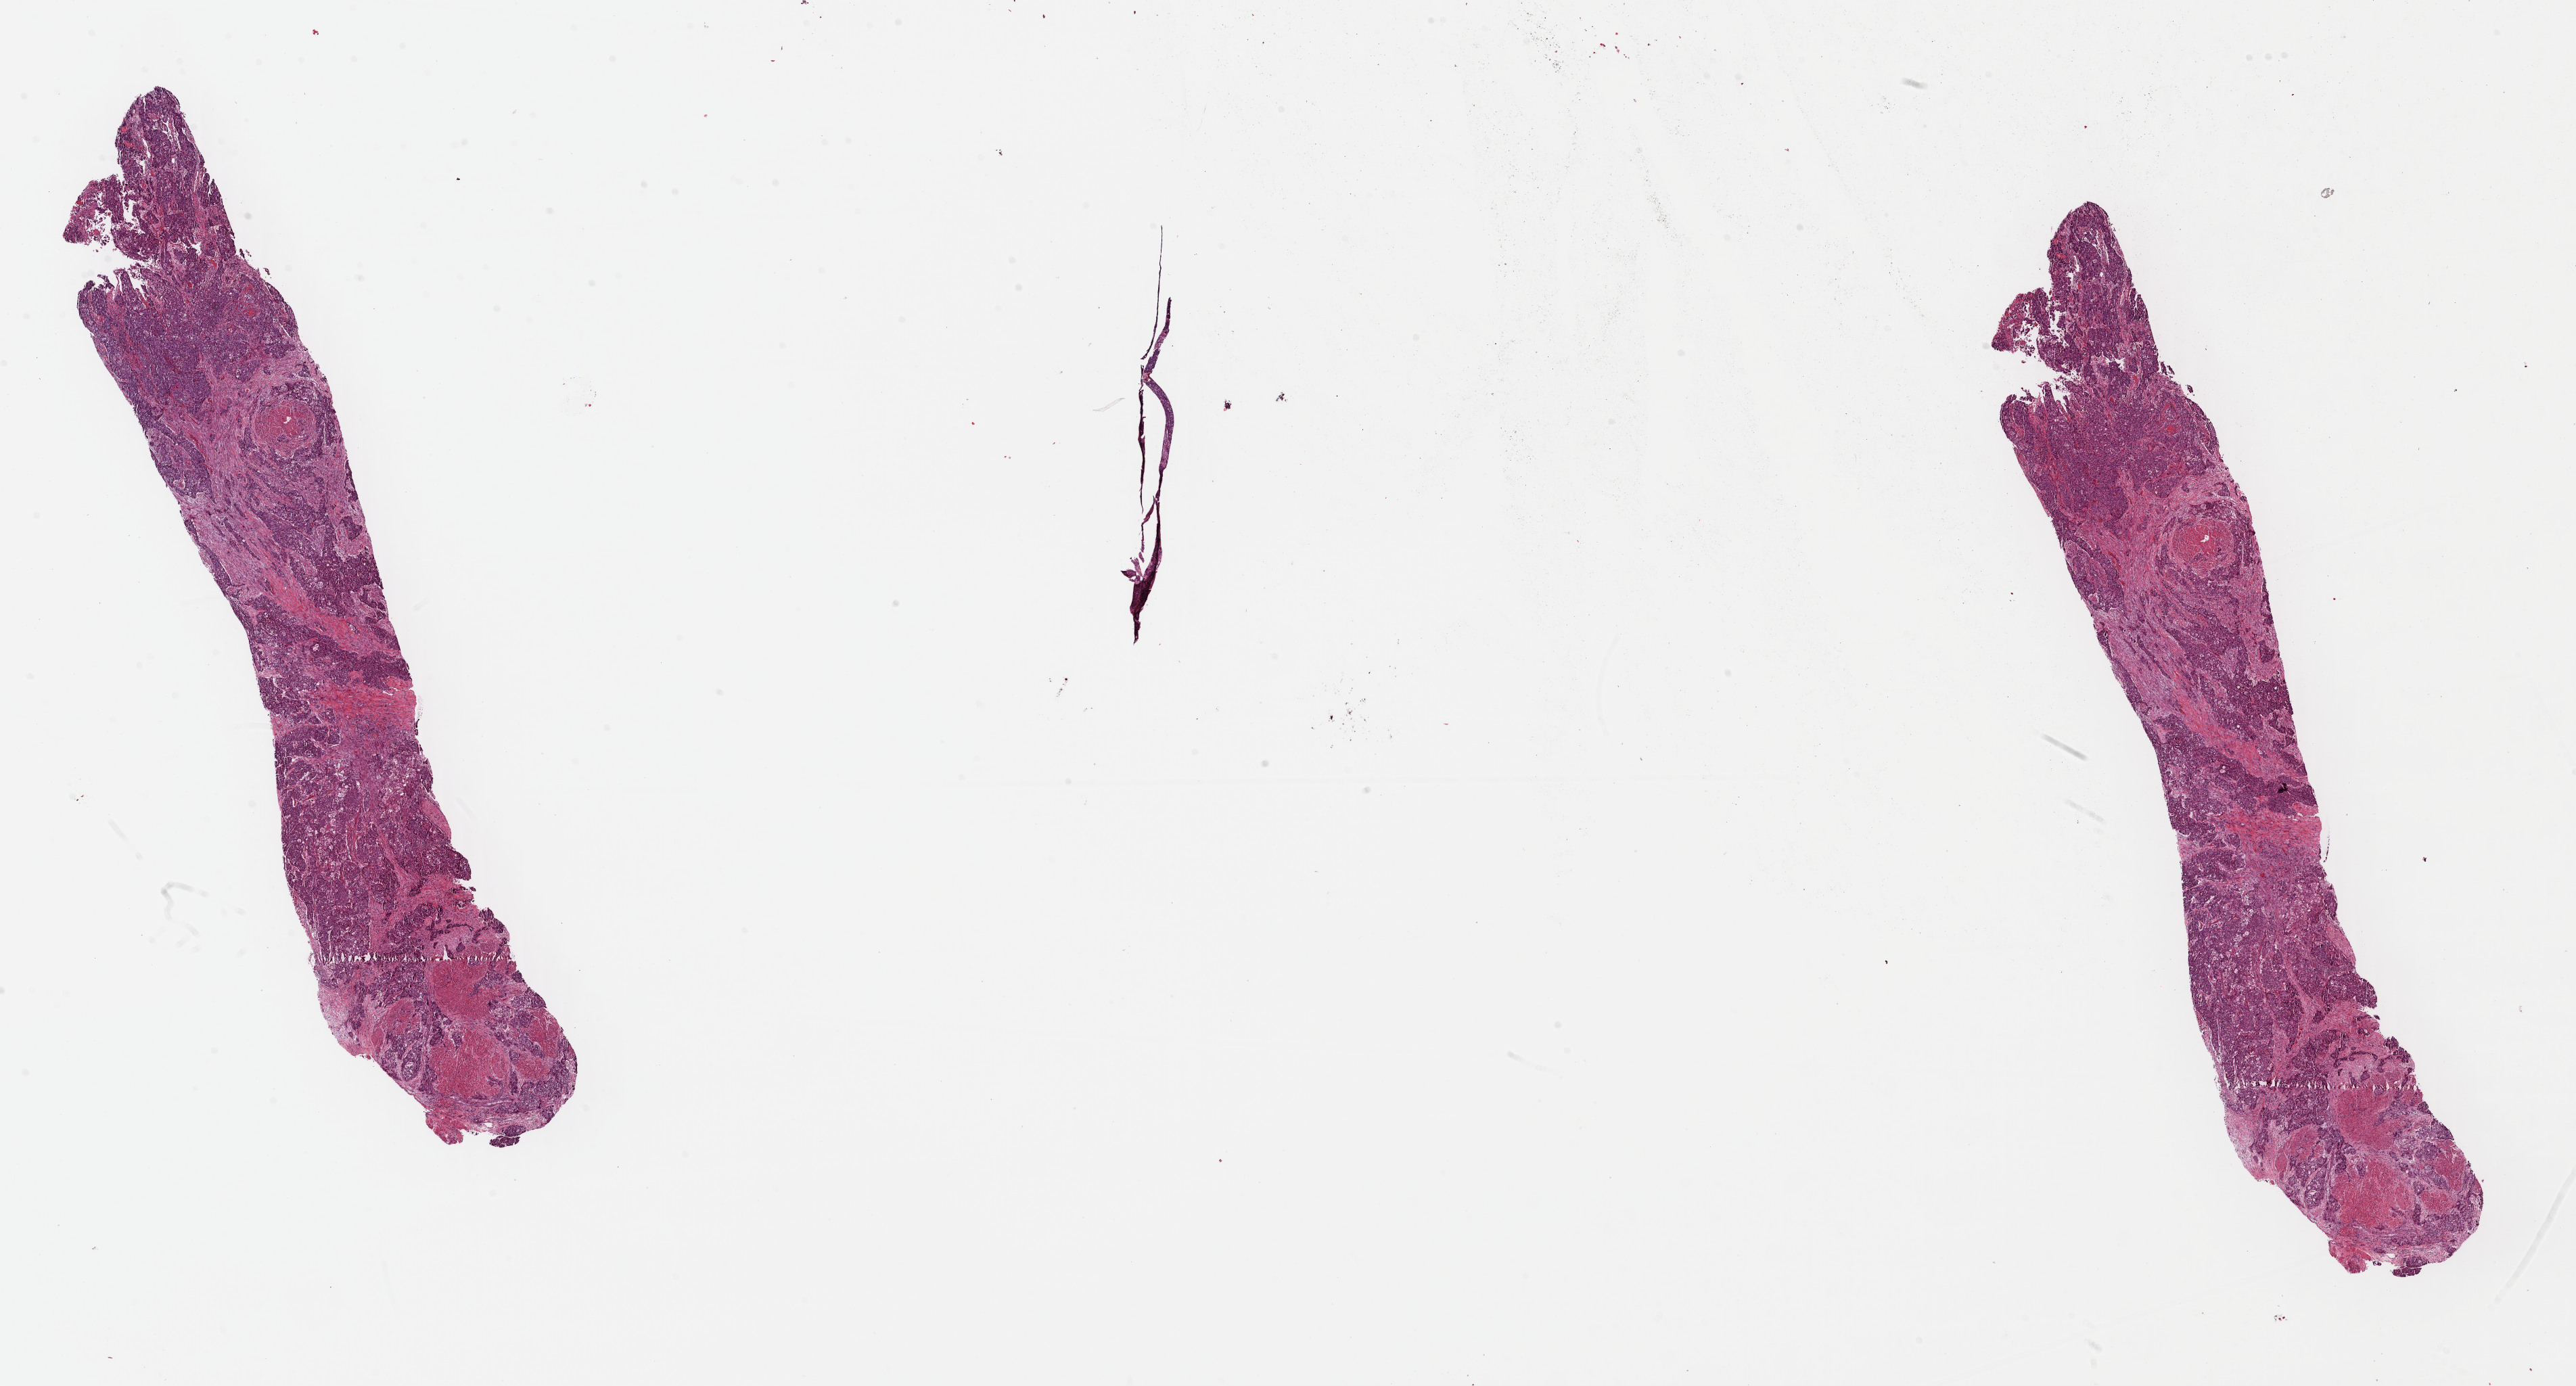
H&E whole-slide image — a low-resolution overview of the entire scanned area, about 29.9 x 16.1 mm (from a 40x scan); formalin-fixed paraffin-embedded (FFPE) diagnostic section; bladder, primary tumour sample. Patient: male, age at initial diagnosis 65 years. Histologic grade: high grade.
- AJCC pathologic stage: IV
- TNM: T4 N2 M0
- pathologic diagnosis: Transitional cell carcinoma (posterior wall of bladder)